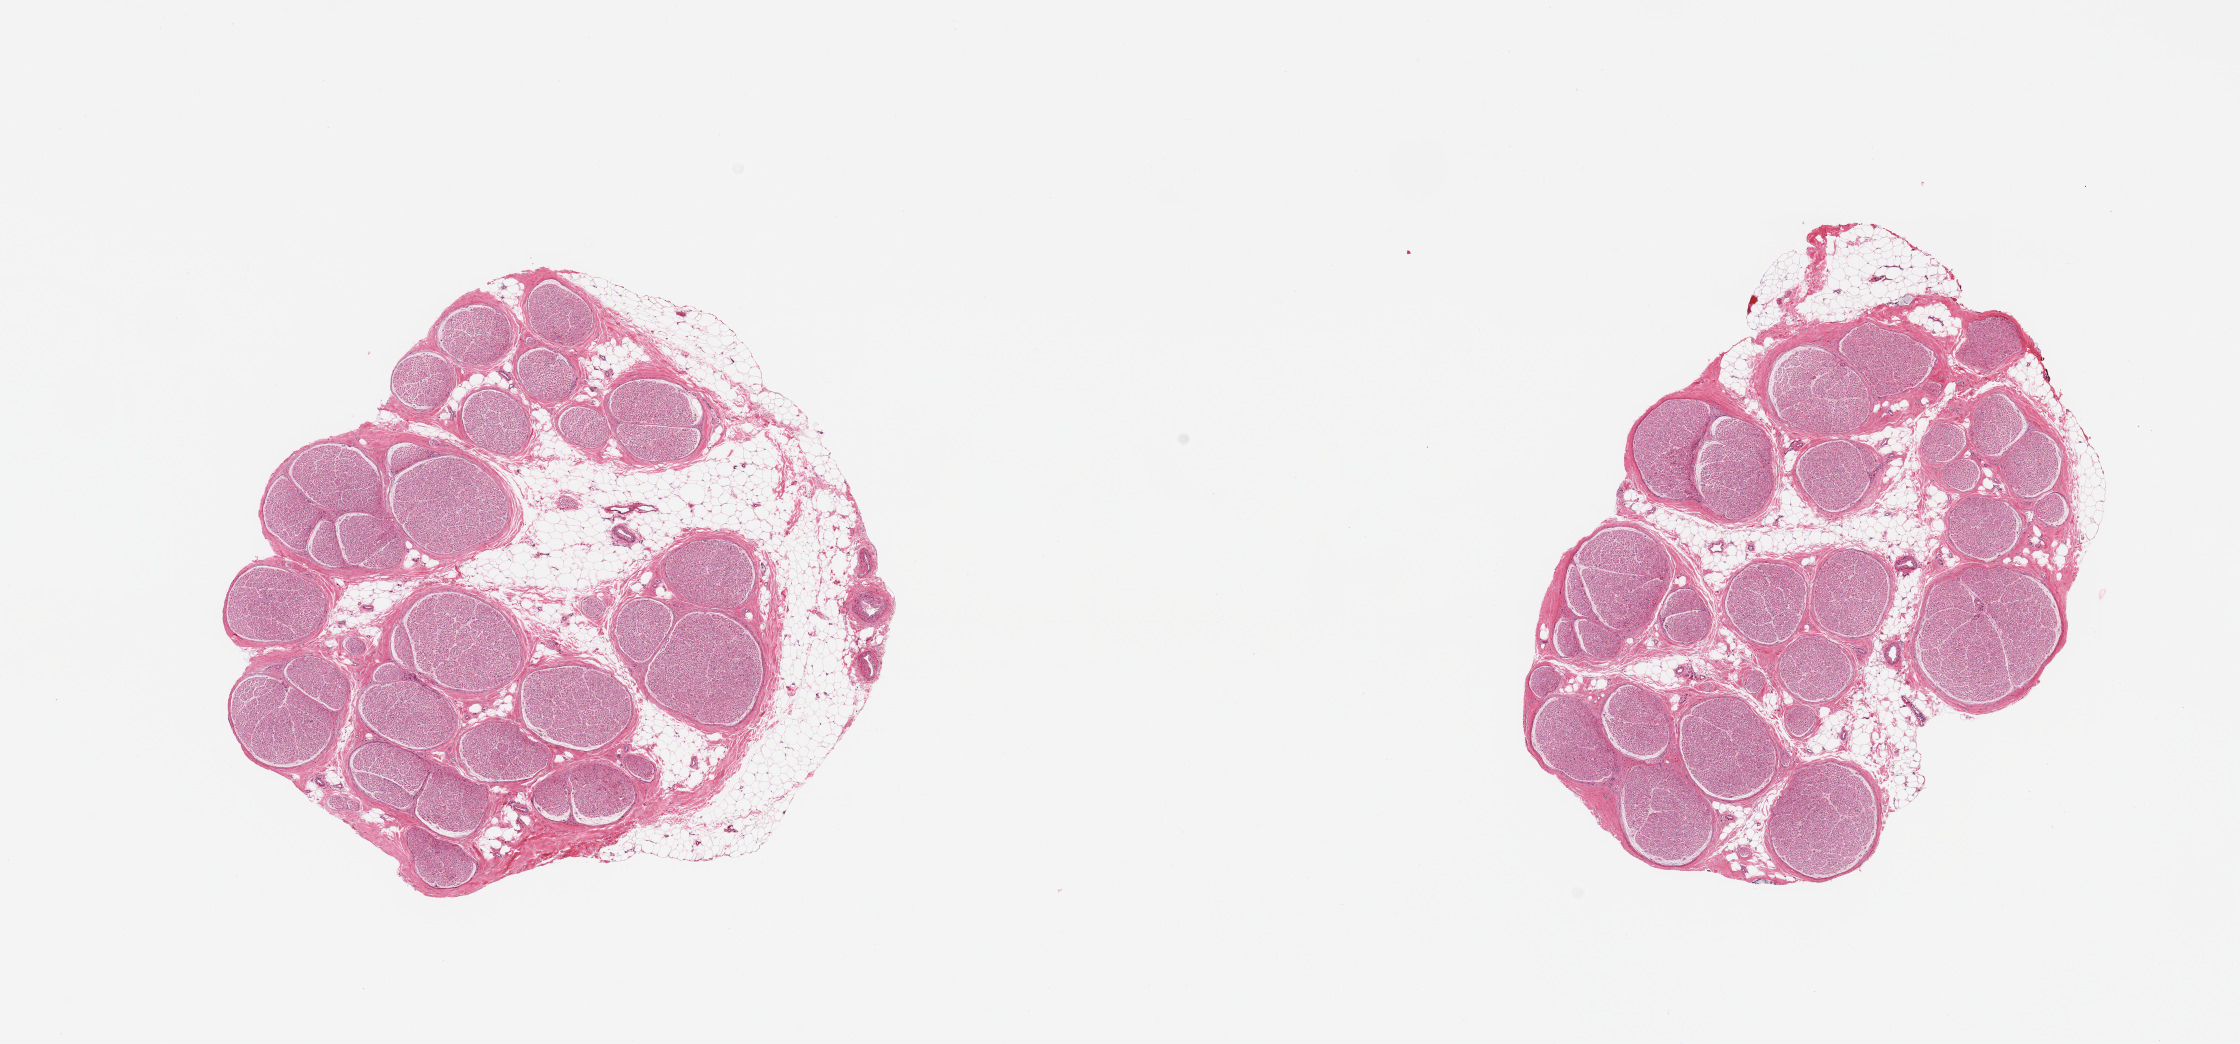
Whole-slide image, haematoxylin and eosin stain — low-resolution overview of the scanned area, about 17.7 x 8.3 mm, PAXgene-fixed, paraffin-embedded tissue, sampled site (target tissue): tibial nerve, tissue donor sample. Female donor.
Review note (as recorded): 2 pieces trace rims of adherent fat up to ~1mm.